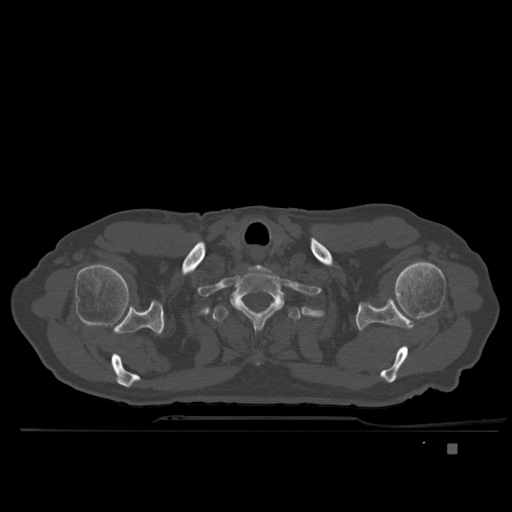
CT including the spine, one axial slice; position 322 of 435 along the scan axis; bone window (W 1800 / L 400 HU); 1.5 mm slice thickness; 512 × 512 image matrix. Male patient, age 73 years. From the clinical record (not read from this slice): primary cancer: skin.
Structures marked on this image (semi-automatic segmentation, software-assisted and operator-edited):
- T1 vertebra: box from (x=229, y=268) to (x=285, y=336) px
- T2 vertebra: (x=215, y=305)–(x=300, y=324)